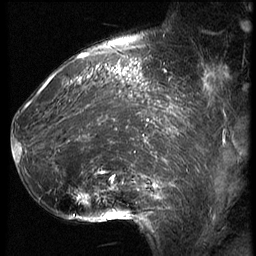
Breast MRI (dynamic contrast-enhanced), one sagittal slice. Position 20 of 62 along the scan axis. 3 images stored at this slice position (order not interpretable as contrast timing). 1.5 T. TE 4.2 ms, TR 9 ms. 256 × 256 image matrix, field of view 180 × 180 mm. Female patient, age 39 years. Case-level facts recorded for this patient, not image findings: setting: breast cancer imaged before/during neoadjuvant chemotherapy; receptor status: HER2-positive.
Annotated regions visible in this slice (semi-automatic segmentation, software-assisted and operator-edited):
- analysis volume of interest (the breast-tissue region the enhancement analysis was run in; not a lesion): box from (x=16, y=64) to (x=171, y=228) px
- tumour enhancement mask (voxels above the 140 % enhancement threshold inside the analysis volume of interest): (x=16, y=65)–(x=171, y=205)